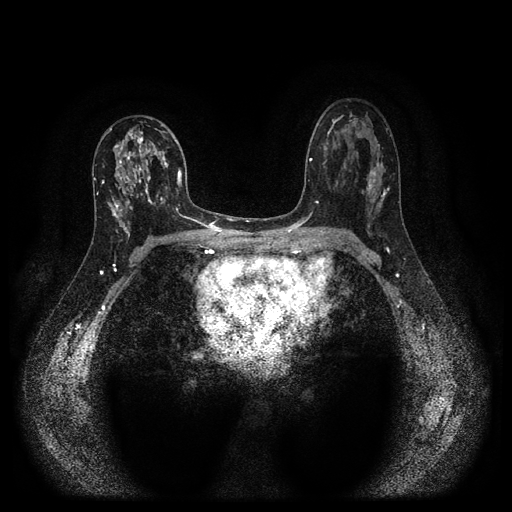
Breast MRI (dynamic contrast-enhanced, multi-phase), one axial slice. Slice 60 of 116 in the series (ordered by position). Dynamic contrast-enhanced series, time point 2 of 5 at this slice position (early post-contrast). 1.5 T. TE 2.7 ms, TR 5.4 ms. 2 mm slice thickness. 512 × 512 image matrix, field of view 330 × 330 mm. Female patient, age 47 years.
Structures marked on this image (semi-automatically segmented with operator editing):
- breast lesion (labelled 'tumour' in the annotation; benign lesions carry a separate 'benign' label): bounding box (x1, y1, x2, y2) in pixels: (113, 128, 171, 229)